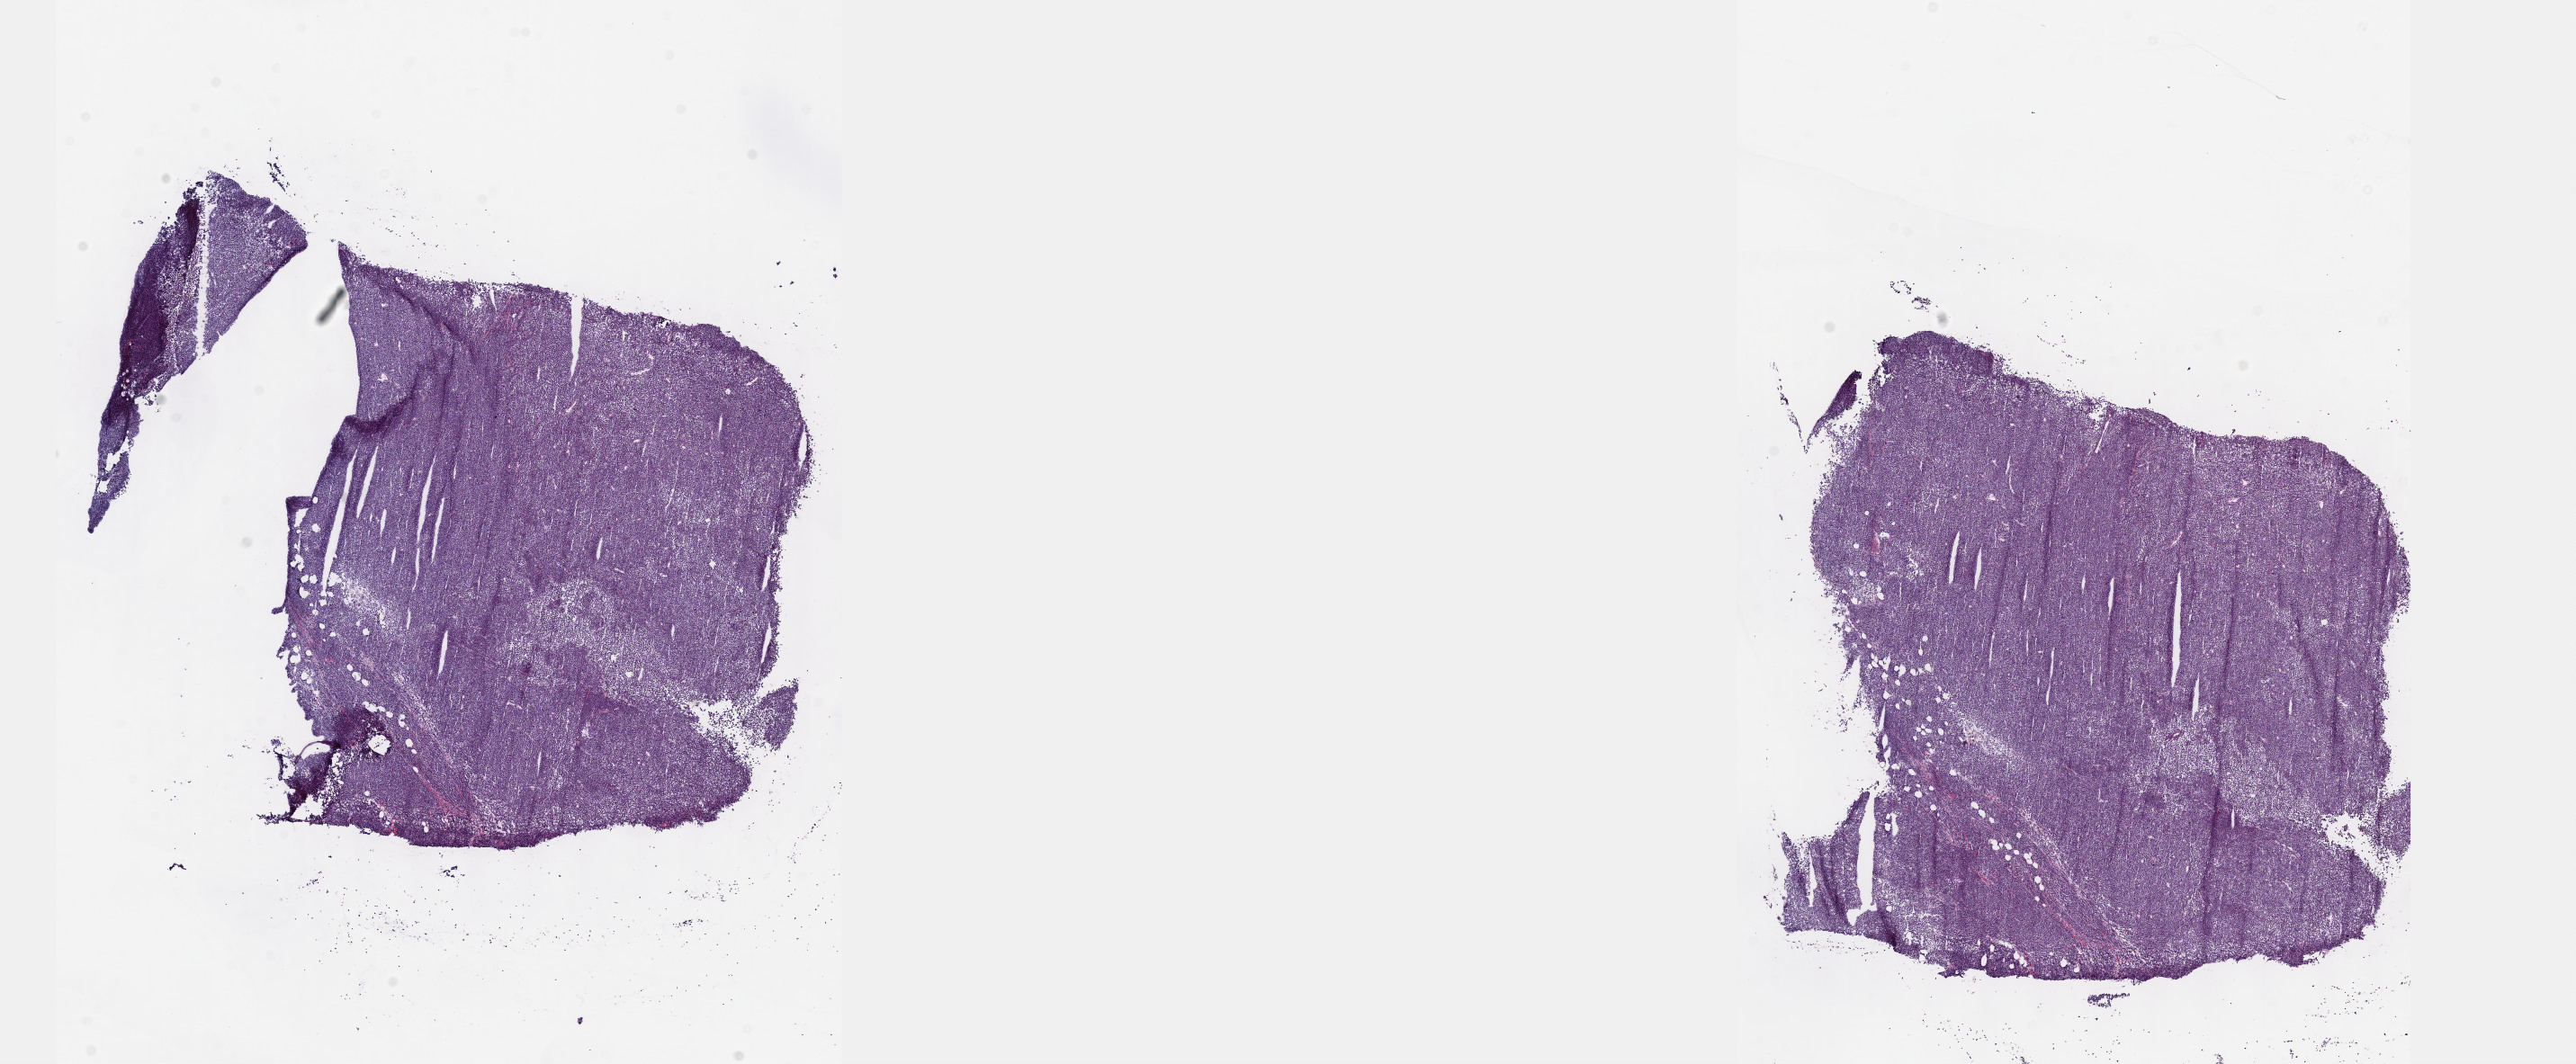
Digitized Hematoxylin and eosin (H&E) stained tissue section (whole slide), low-resolution overview of the scanned area, about 23.1 x 9.6 mm (acquisition: 40x scan); frozen section; metastatic tumour sample, sampled site not recorded. Male, age 58 years at initial diagnosis. Slide review estimates, as recorded: tumour cells 80%, tumour nuclei 80%, normal cells 0%, stromal cells 20%, necrosis 0%. Infiltration values recorded for this section: lymphocyte infiltration 3%, monocyte infiltration 0%, neutrophil infiltration 0%.
- this section: metastatic tumour tissue
- patient diagnosis: Malignant melanoma, NOS